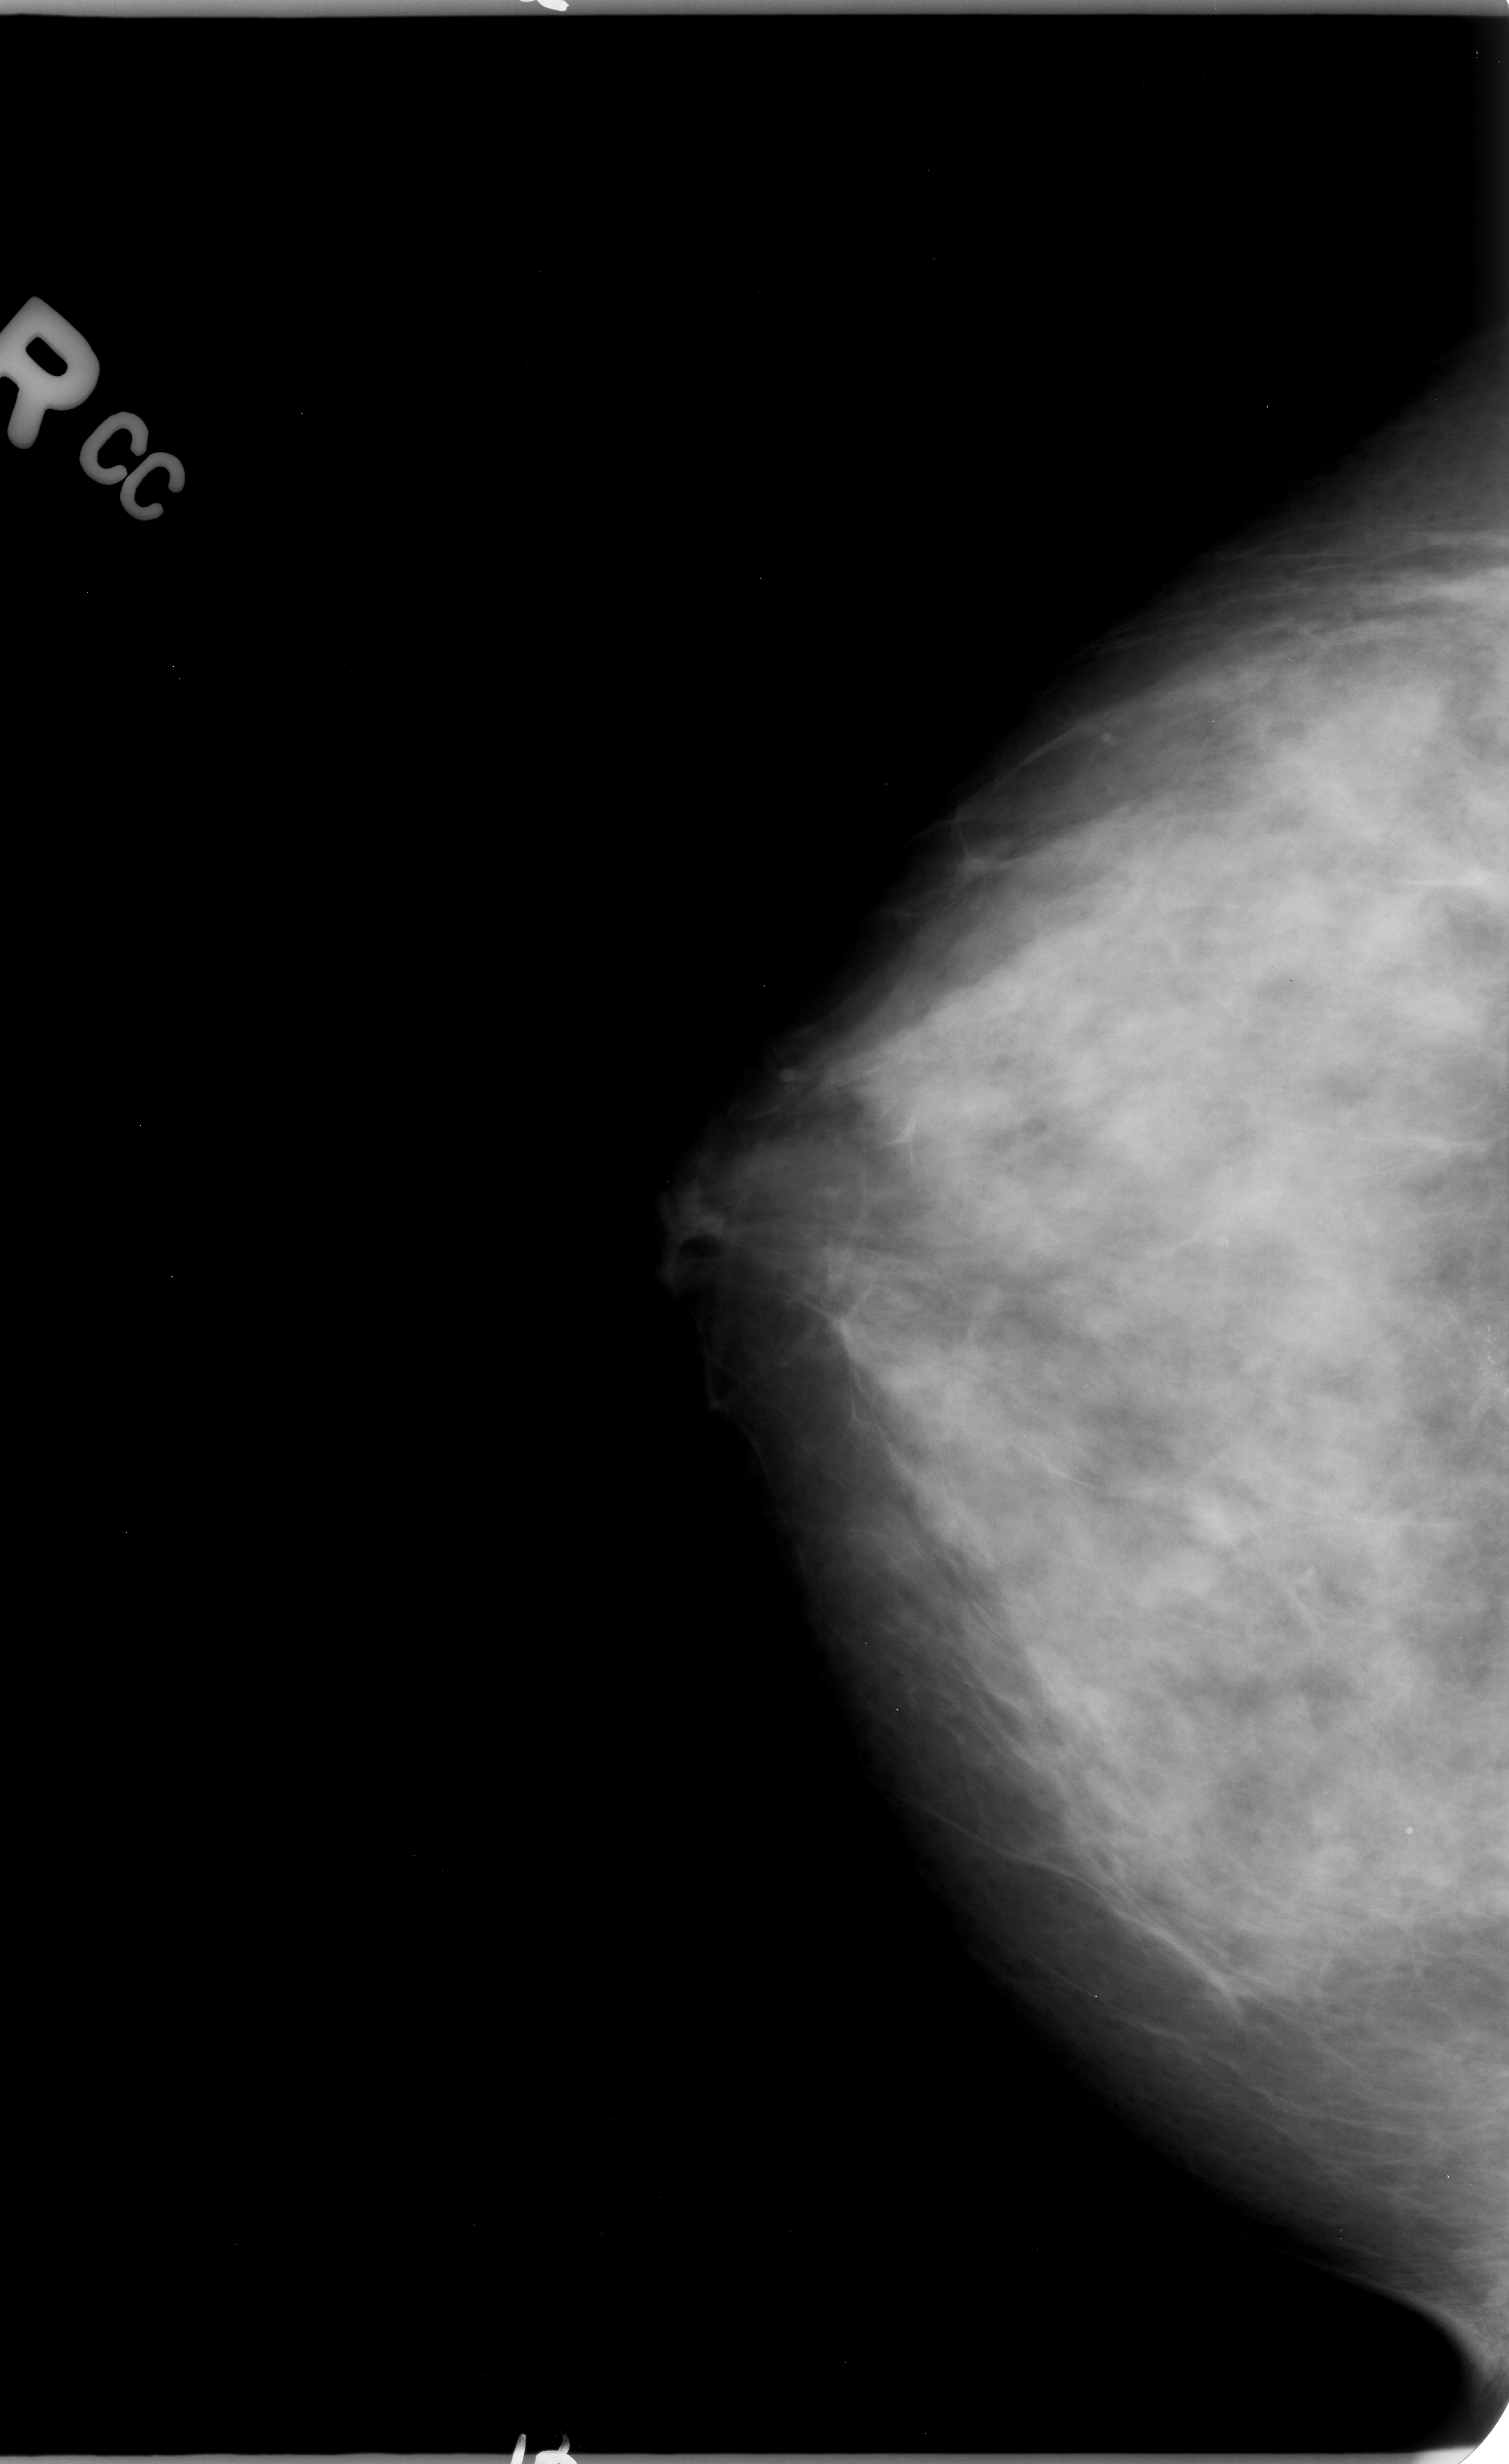
Scanned film-screen mammogram, right breast, craniocaudal (CC) view.
- Radiologist-marked abnormalities on this image: calcifications, morphology pleomorphic, distribution clustered; BI-RADS assessment category 4; subtlety rating 4 on a 1 (subtle) to 5 (obvious) scale; pathology result (as recorded, not read from the image): malignant.